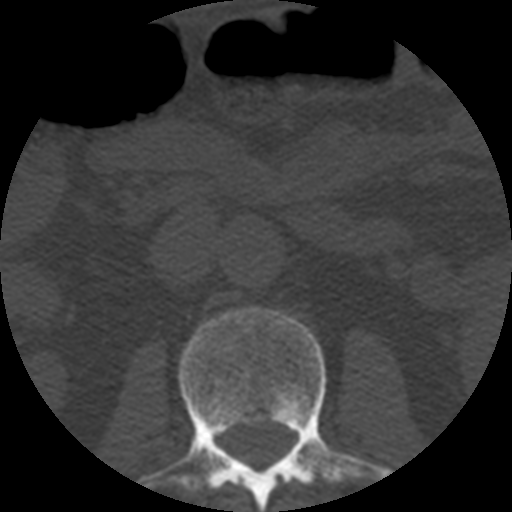
CT including the spine, one axial slice; slice 152 of 508 in the series (ordered by position); reconstruction kernel STANDARD; 120 kVp; bone window (W 1800 / L 400 HU); 1.25 mm slice thickness; 512 × 512 image matrix, field of view 160 × 160 mm. Patient age 57 years. Case-level facts recorded for this patient, not image findings: primary cancer: prostate.
Structures marked on this image (semi-automatically segmented with operator editing):
- L2 vertebra: bounding box <139,308,392,512> (left, top, right, bottom; pixels)